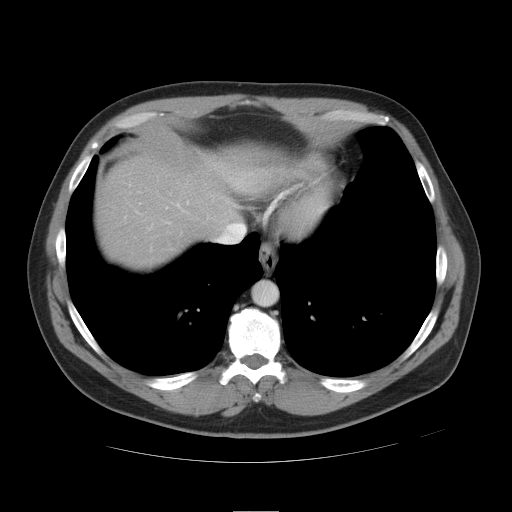
Contrast-enhanced abdominal CT, one axial slice; slice 42 of 49 in the series (ordered by position); intravenous contrast given; soft-tissue window (W 400 / L 40 HU); 512 × 512 image matrix, field of view 425 × 425 mm. Male patient, age 52 years. Case-level facts recorded for this patient, not image findings: diagnosis: colorectal cancer liver metastases, imaged before liver resection; multiple liver metastases: yes; largest metastasis: 5.1 cm; disease in both lobes: yes.
Outlined on this slice (expert manual segmentation):
- hepatic veins: box from (x=224, y=223) to (x=246, y=234) px
- liver: (x=99, y=159)–(x=236, y=268)
- planned liver remnant (the part of the liver to remain after resection): (x=152, y=162)–(x=236, y=227)